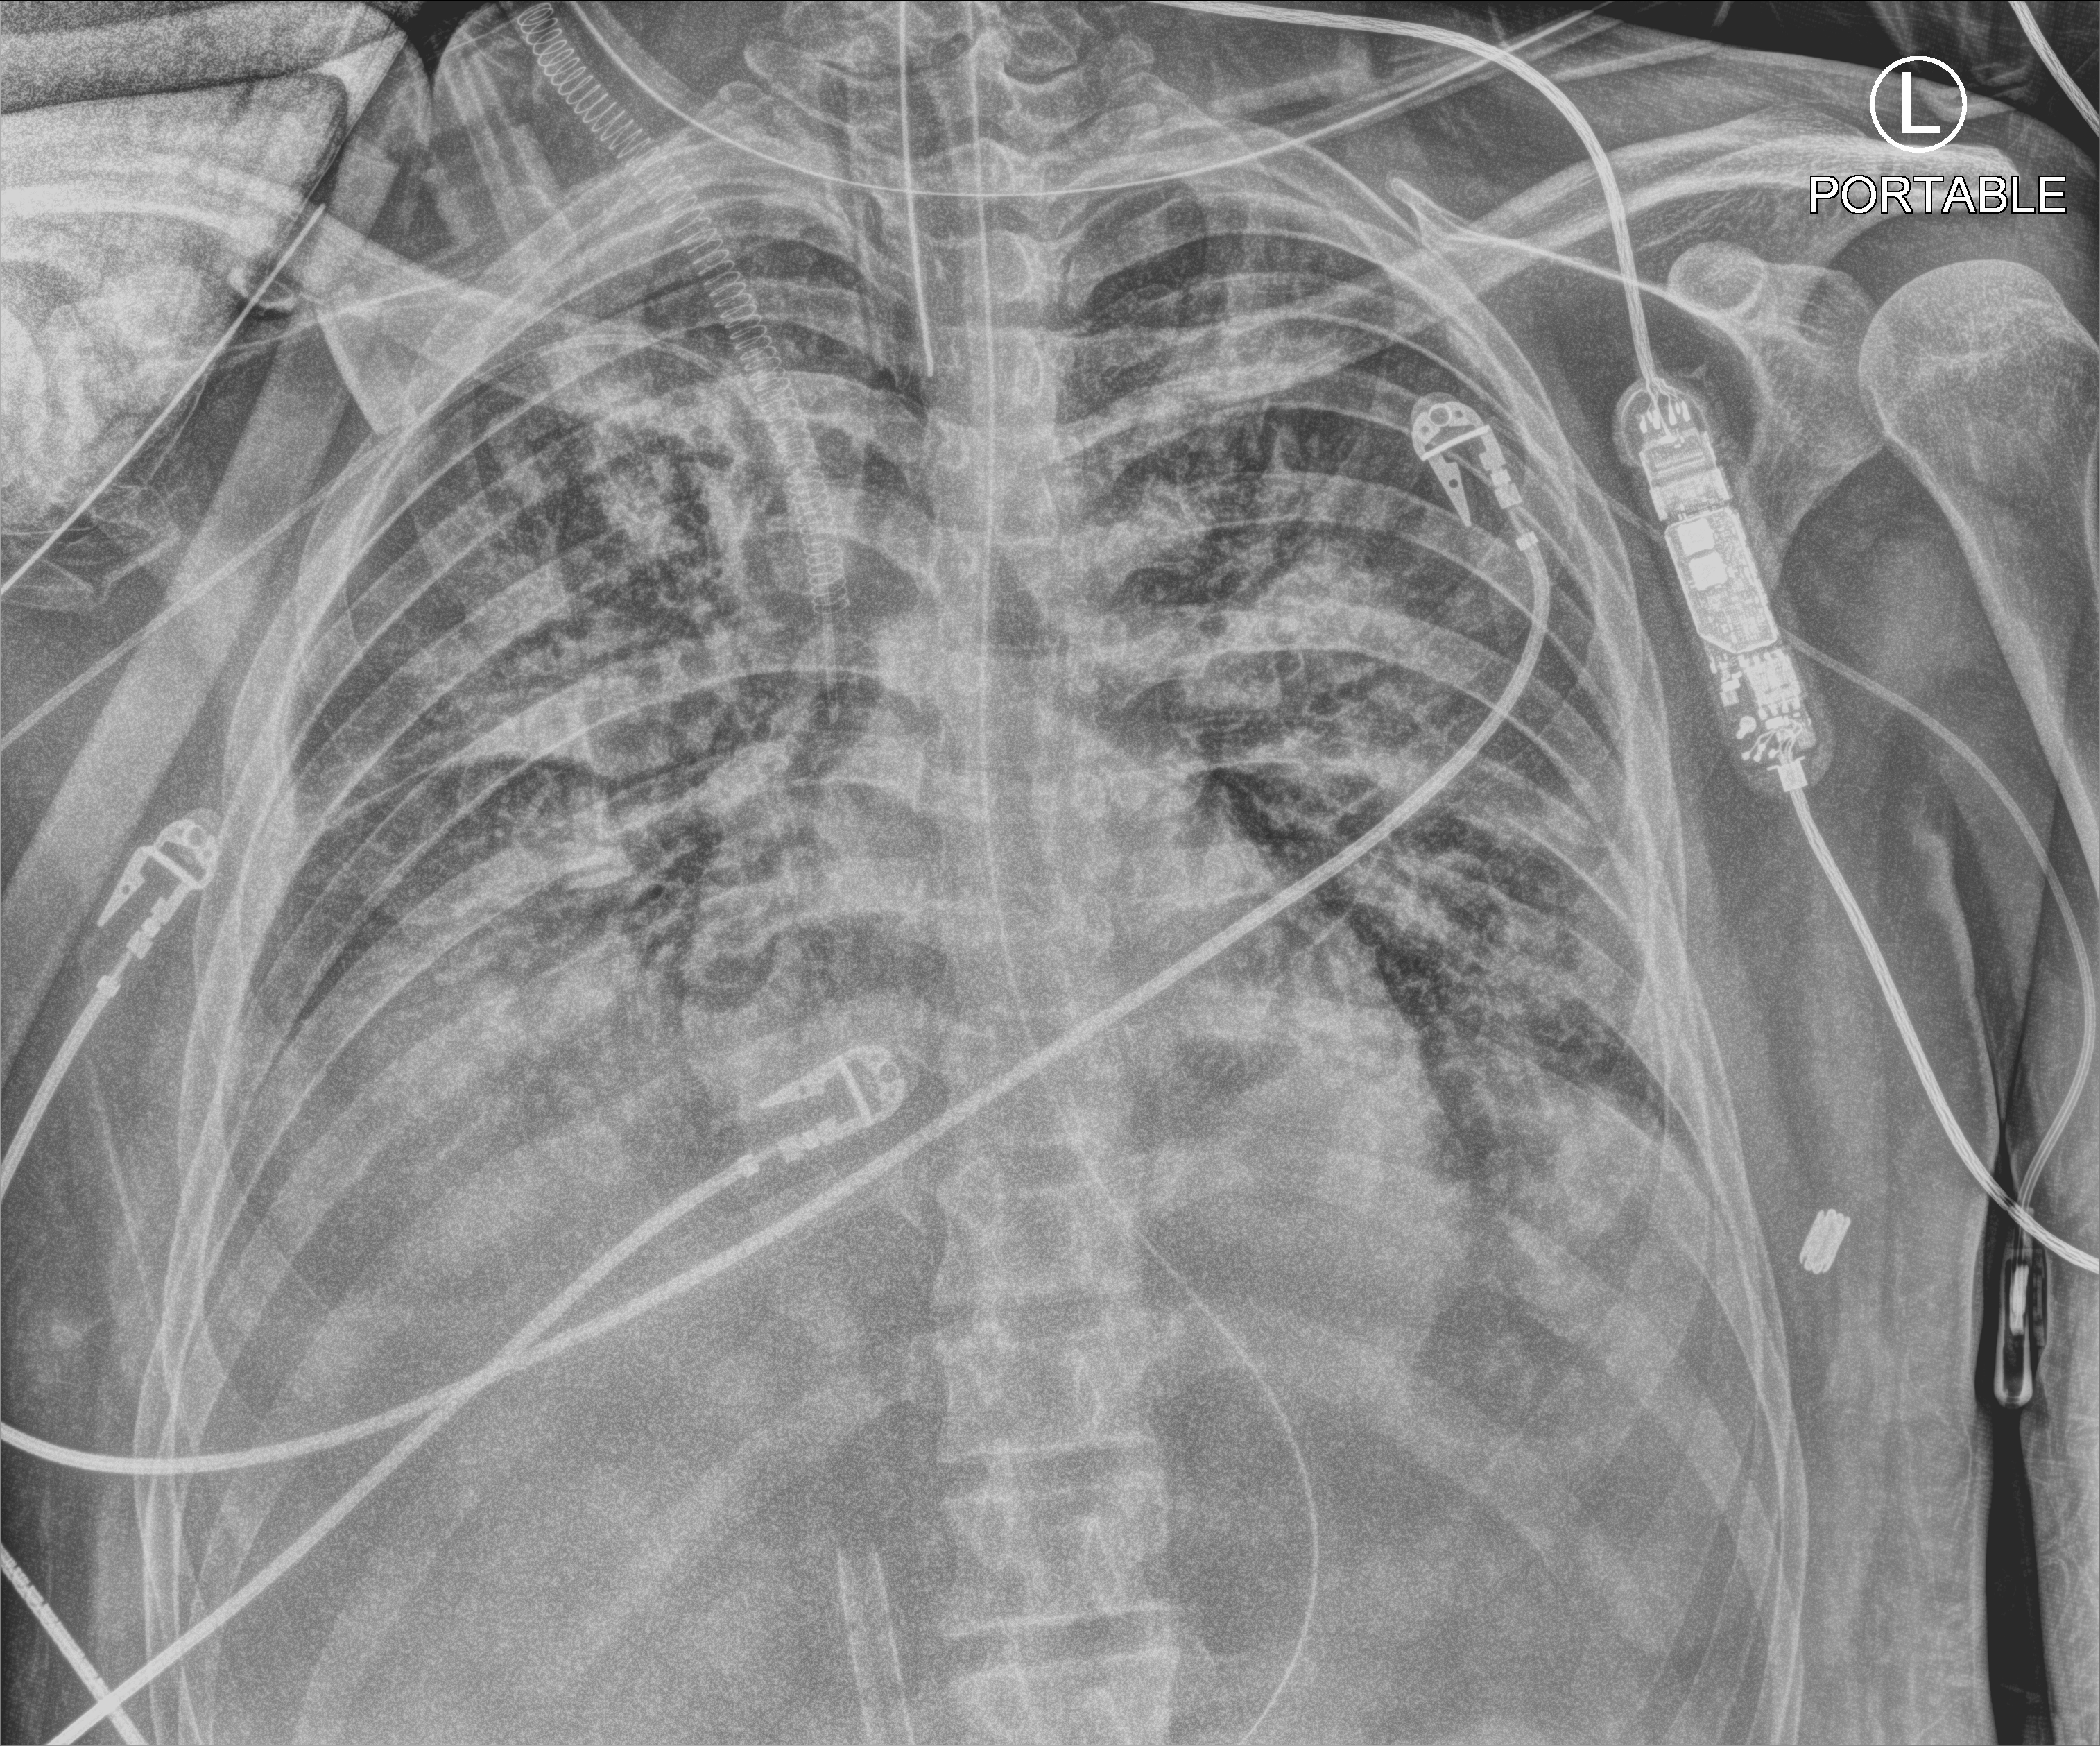
Portable chest radiograph, anteroposterior (AP) projection. Patient hospitalised with COVID-19, aged 18–59 years.
Hospital-stay facts (about this admission, not read from this image; timing relative to this image not recorded): diabetes (admission record): no; mechanically ventilated during this hospital stay: yes; admitted to intensive care during this hospital stay: yes.